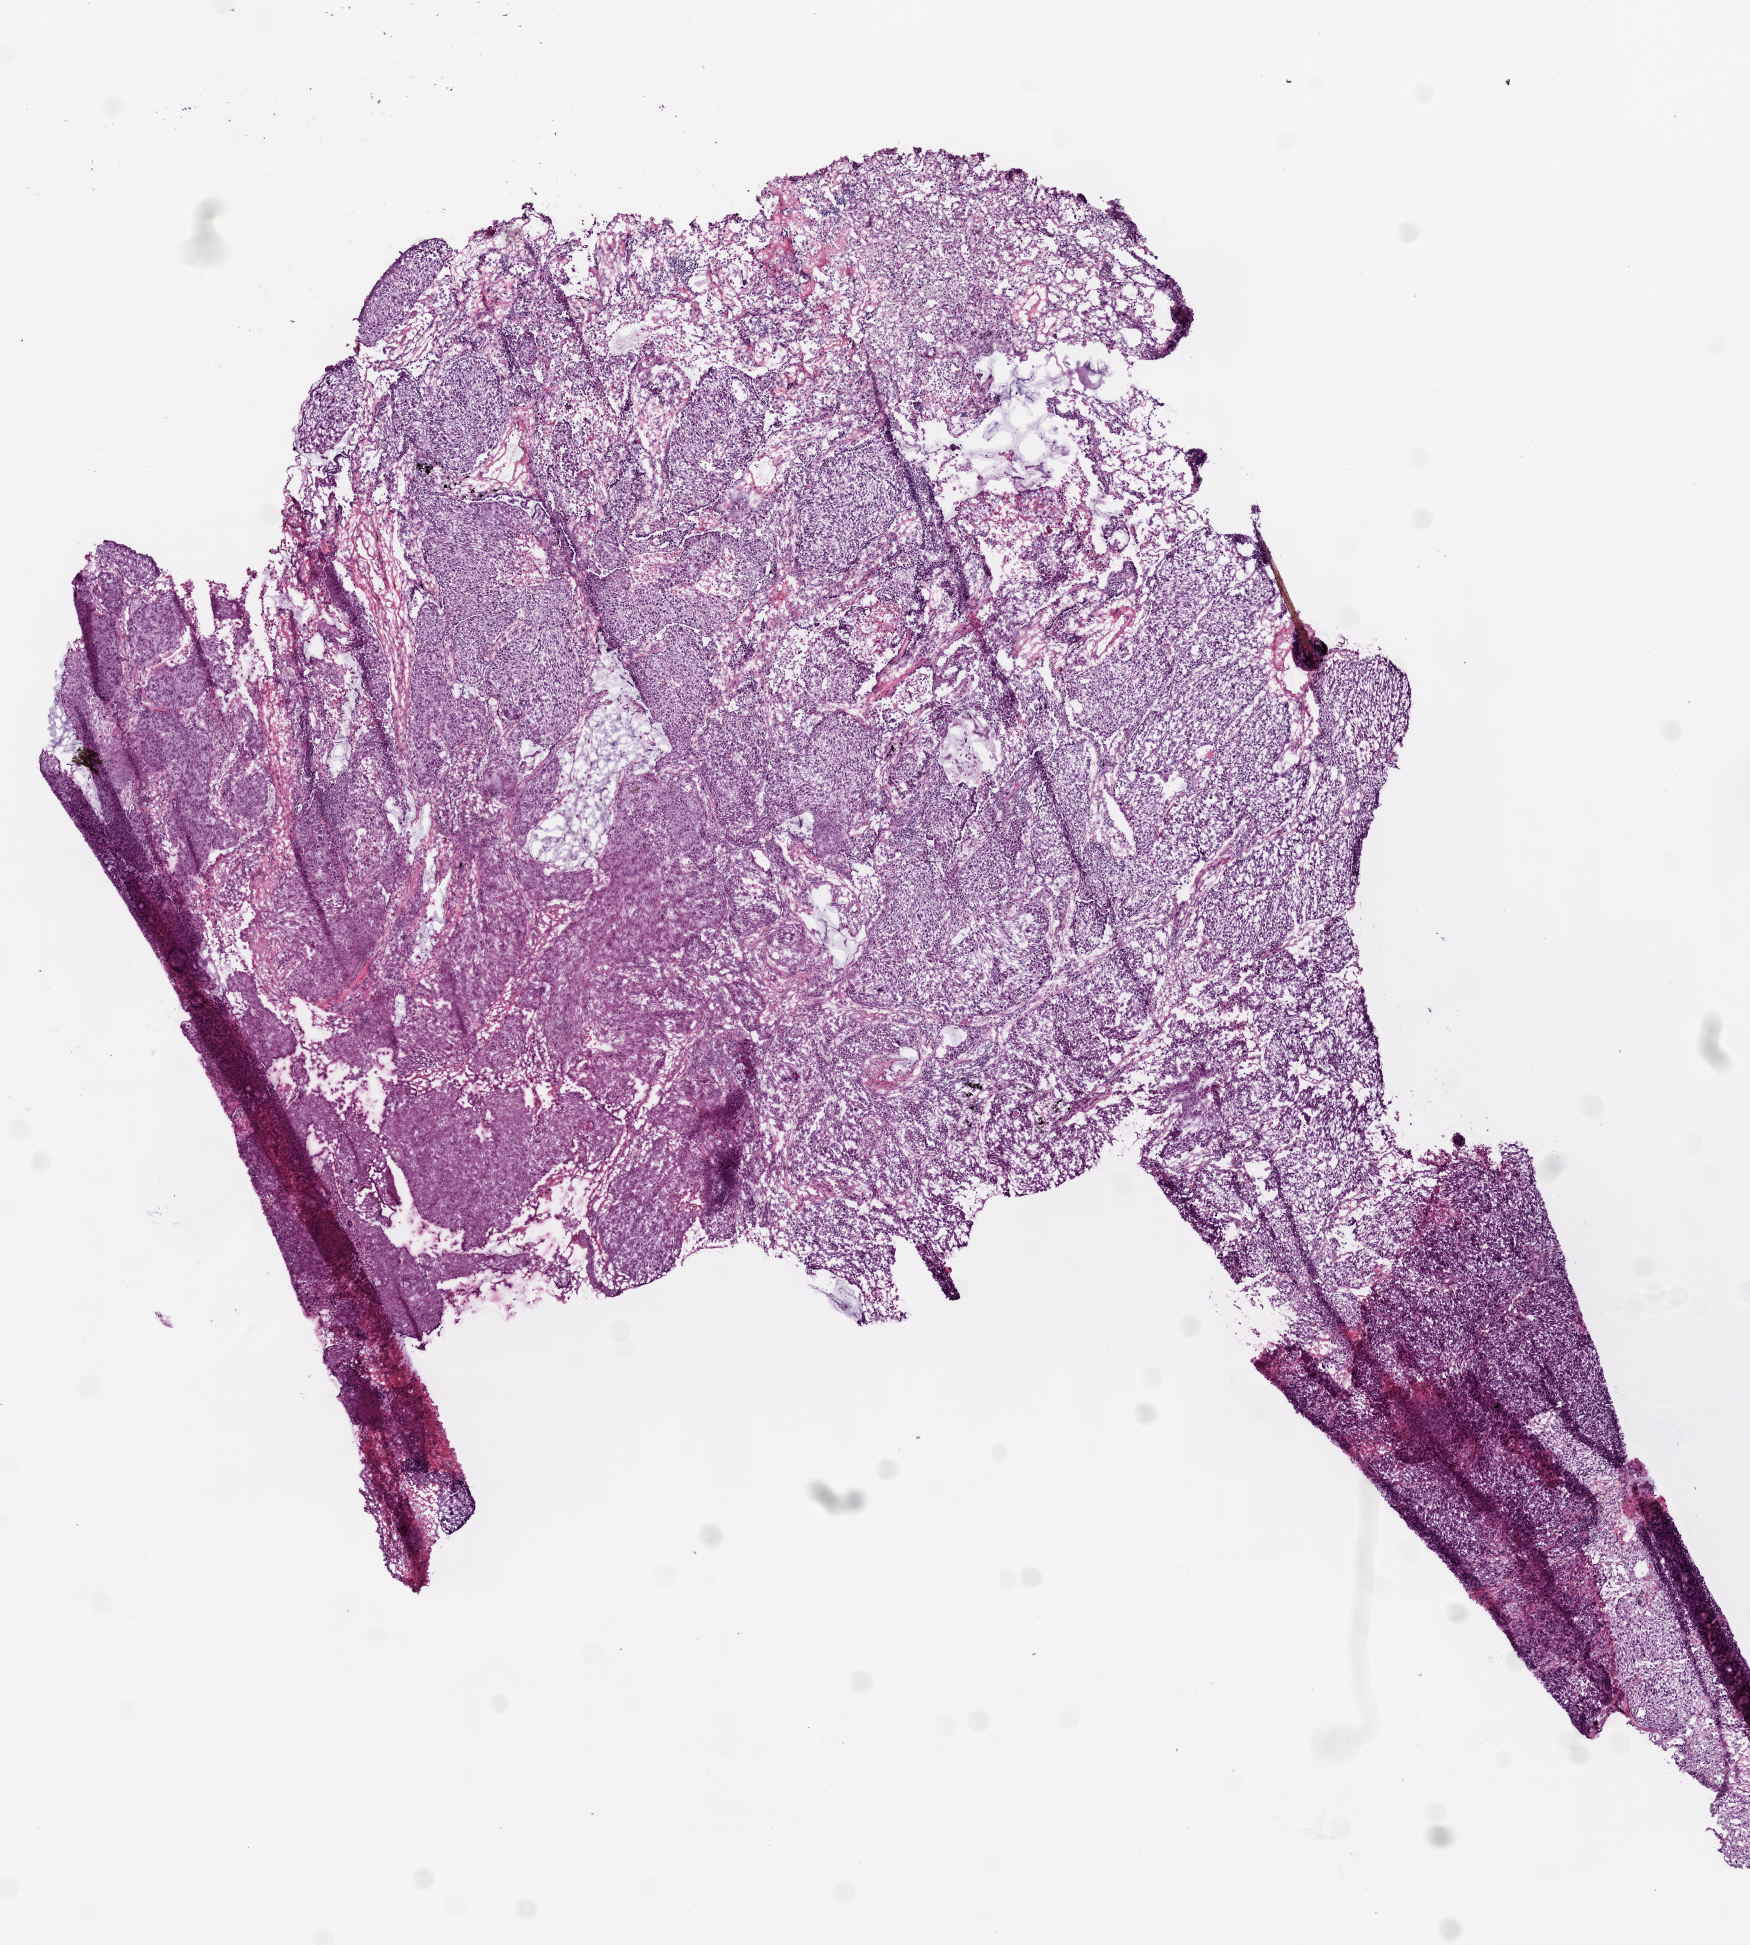
Digitized H&E tissue section (whole slide), shown as a low-resolution overview of the whole scanned area (about 7.0 x 7.8 mm, acquisition: 20x scan). Frozen section from the top of the tissue portion. Sample: primary tumour, lung. Female, age 68 years at initial diagnosis. Composition of this section per pathologist review: tumour cells 91%, tumour nuclei 85%, normal cells 3%, stromal cells 5%, necrosis 1%.
AJCC pathologic stage: IA (5th edition). Histologic diagnosis: Squamous cell carcinoma, NOS (upper lobe, lung). Laterality: right.